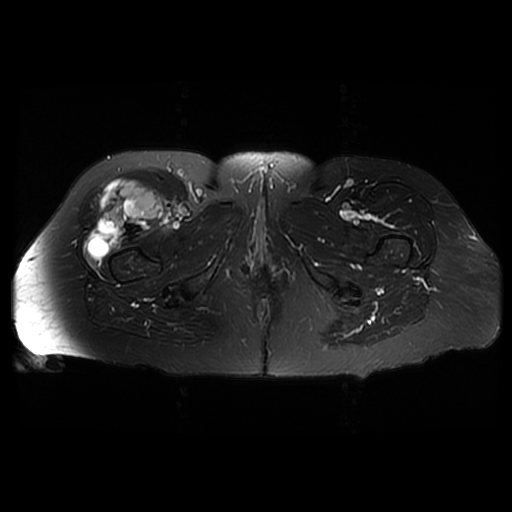
MRI of an extremity soft-tissue mass, one axial slice. Position 31 of 42 along the scan axis. T2-weighted fat-saturated. 6 mm slice thickness. 512 × 512 image matrix, field of view 440 × 440 mm. Female patient. From the clinical record (not read from this slice): histological type: pleiomorphic undifferentiated sarcoma; grade: high; site of the primary tumour: right quadricep.
Outlined on this slice (manually delineated by an expert):
- gross tumour volume including surrounding oedema: bounding box <87,180,163,258> (left, top, right, bottom; pixels)
- gross tumour volume (mass): <87,180,163,258>